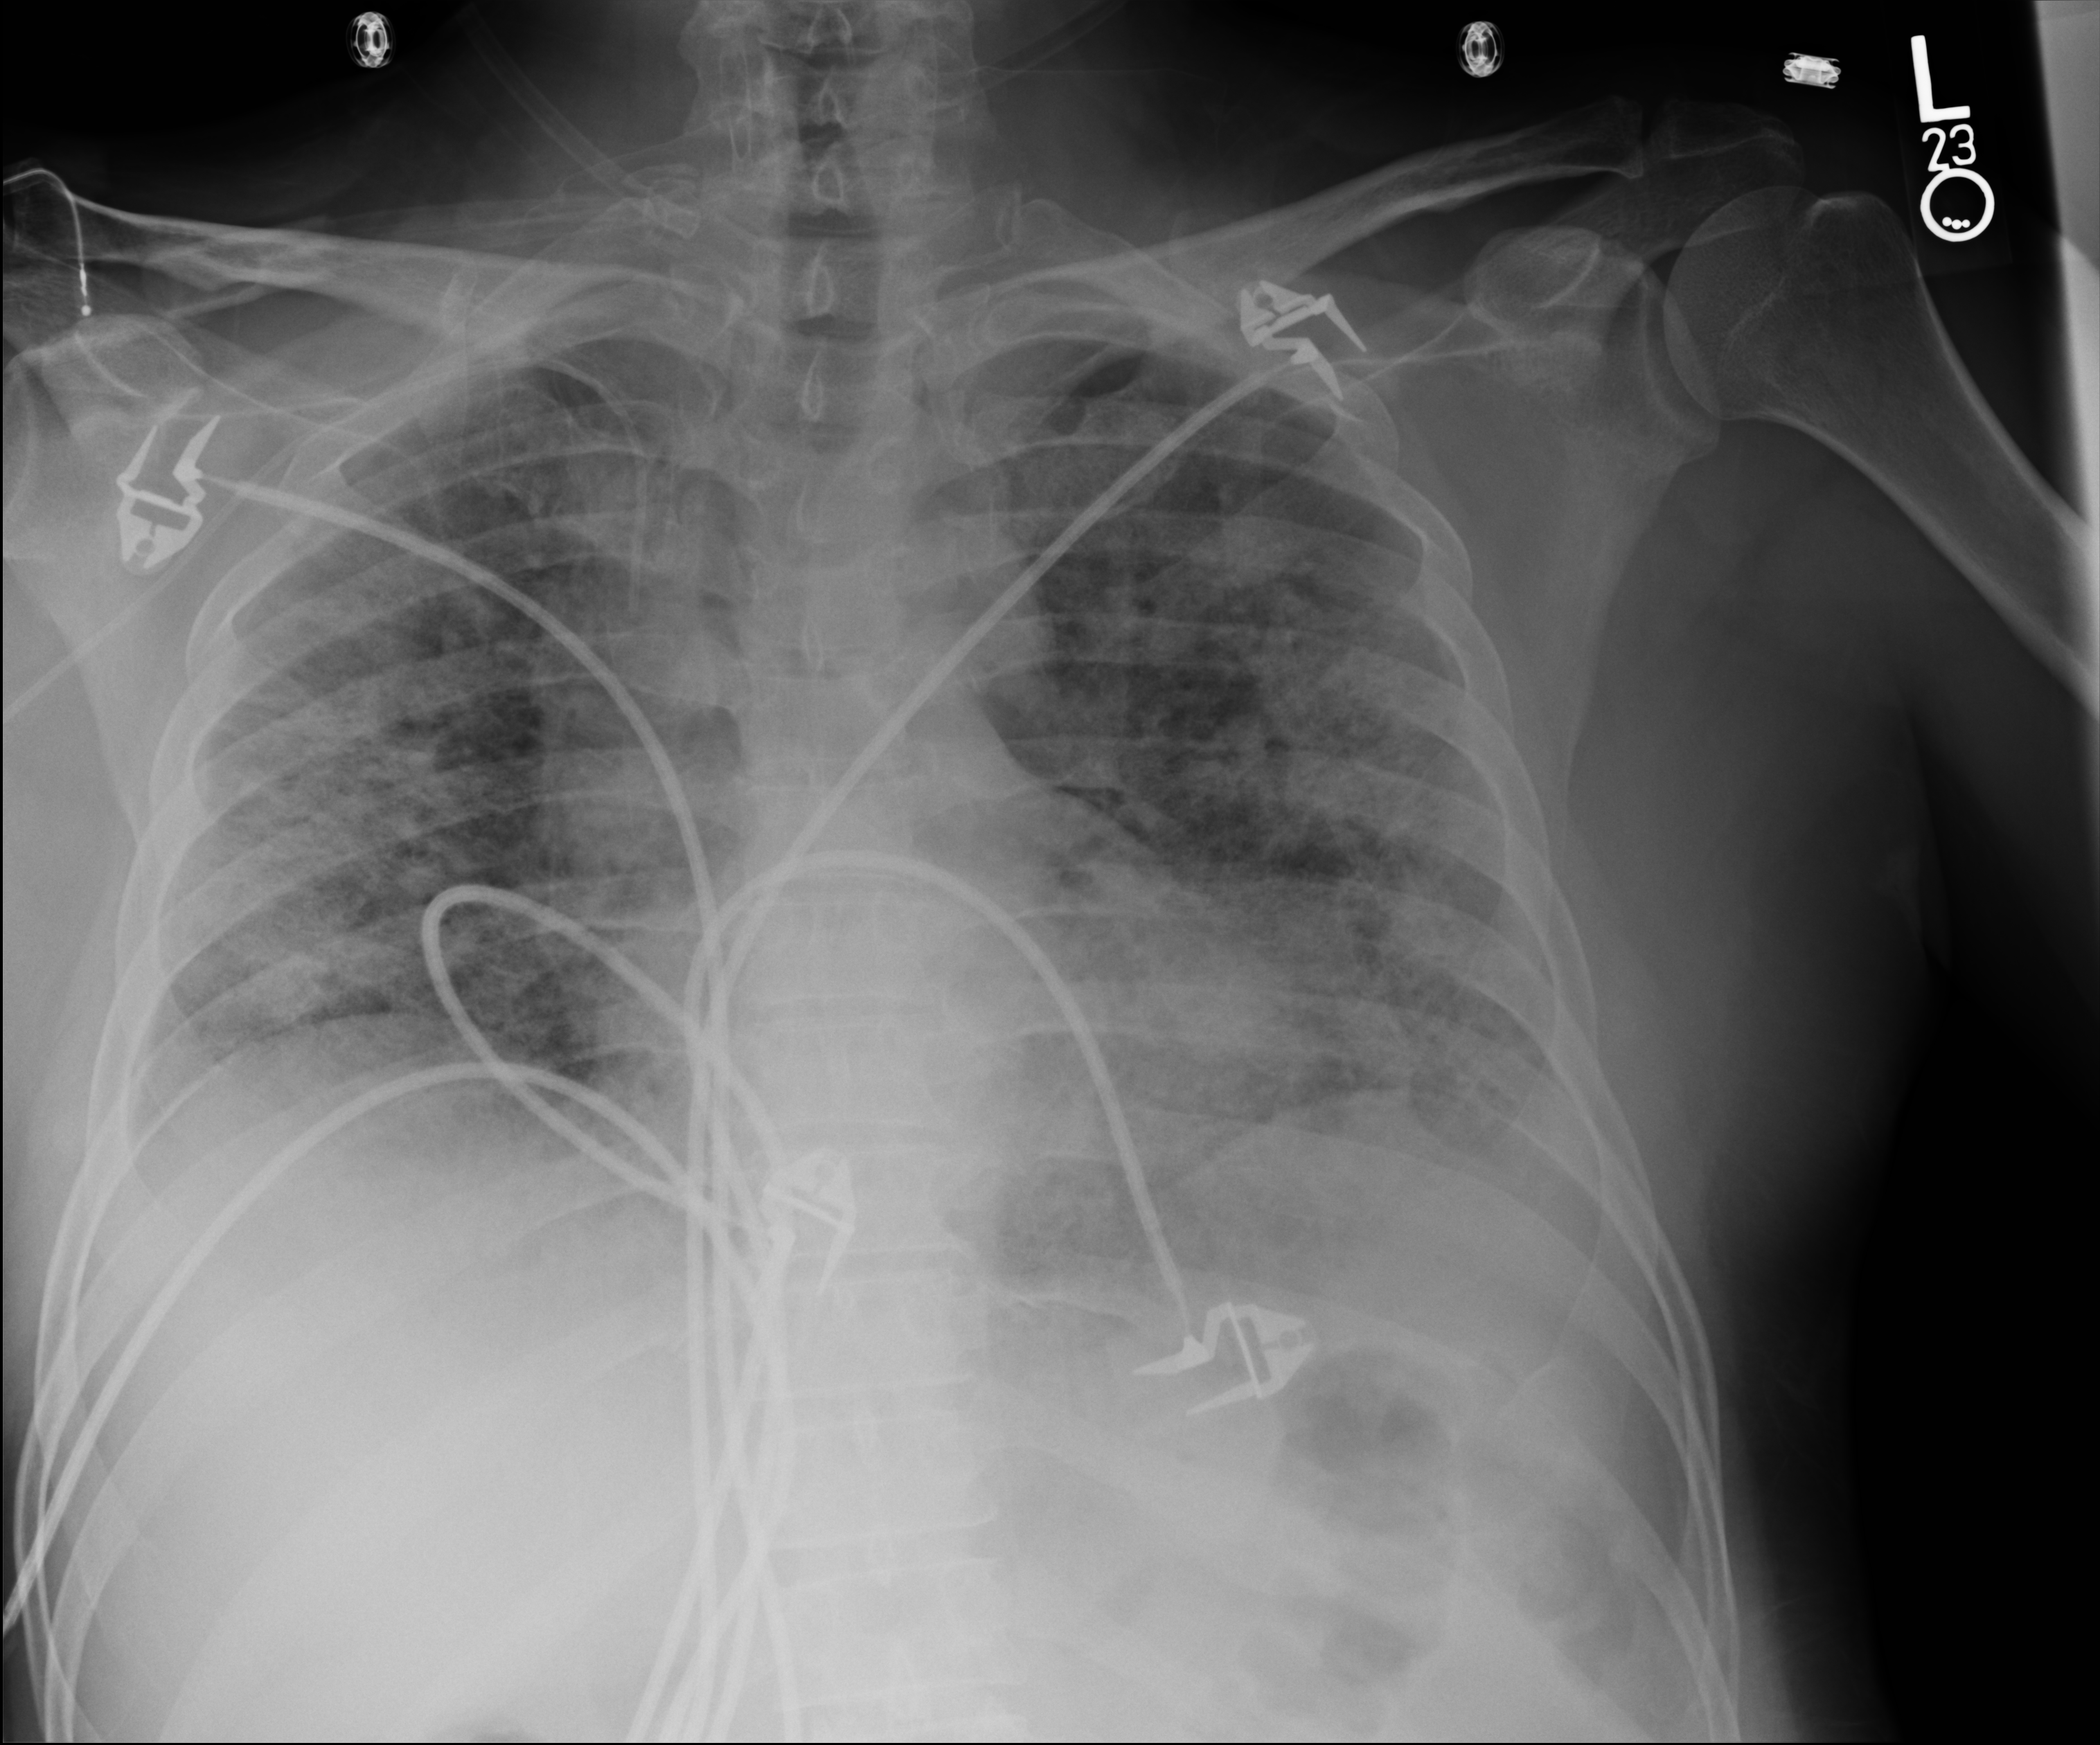
Chest X-ray (portable). Patient hospitalised with COVID-19; male, aged 18–59 years.
Hospital-stay facts (about this admission, not read from this image; timing relative to this image not recorded):
- mechanically ventilated during this hospital stay: yes